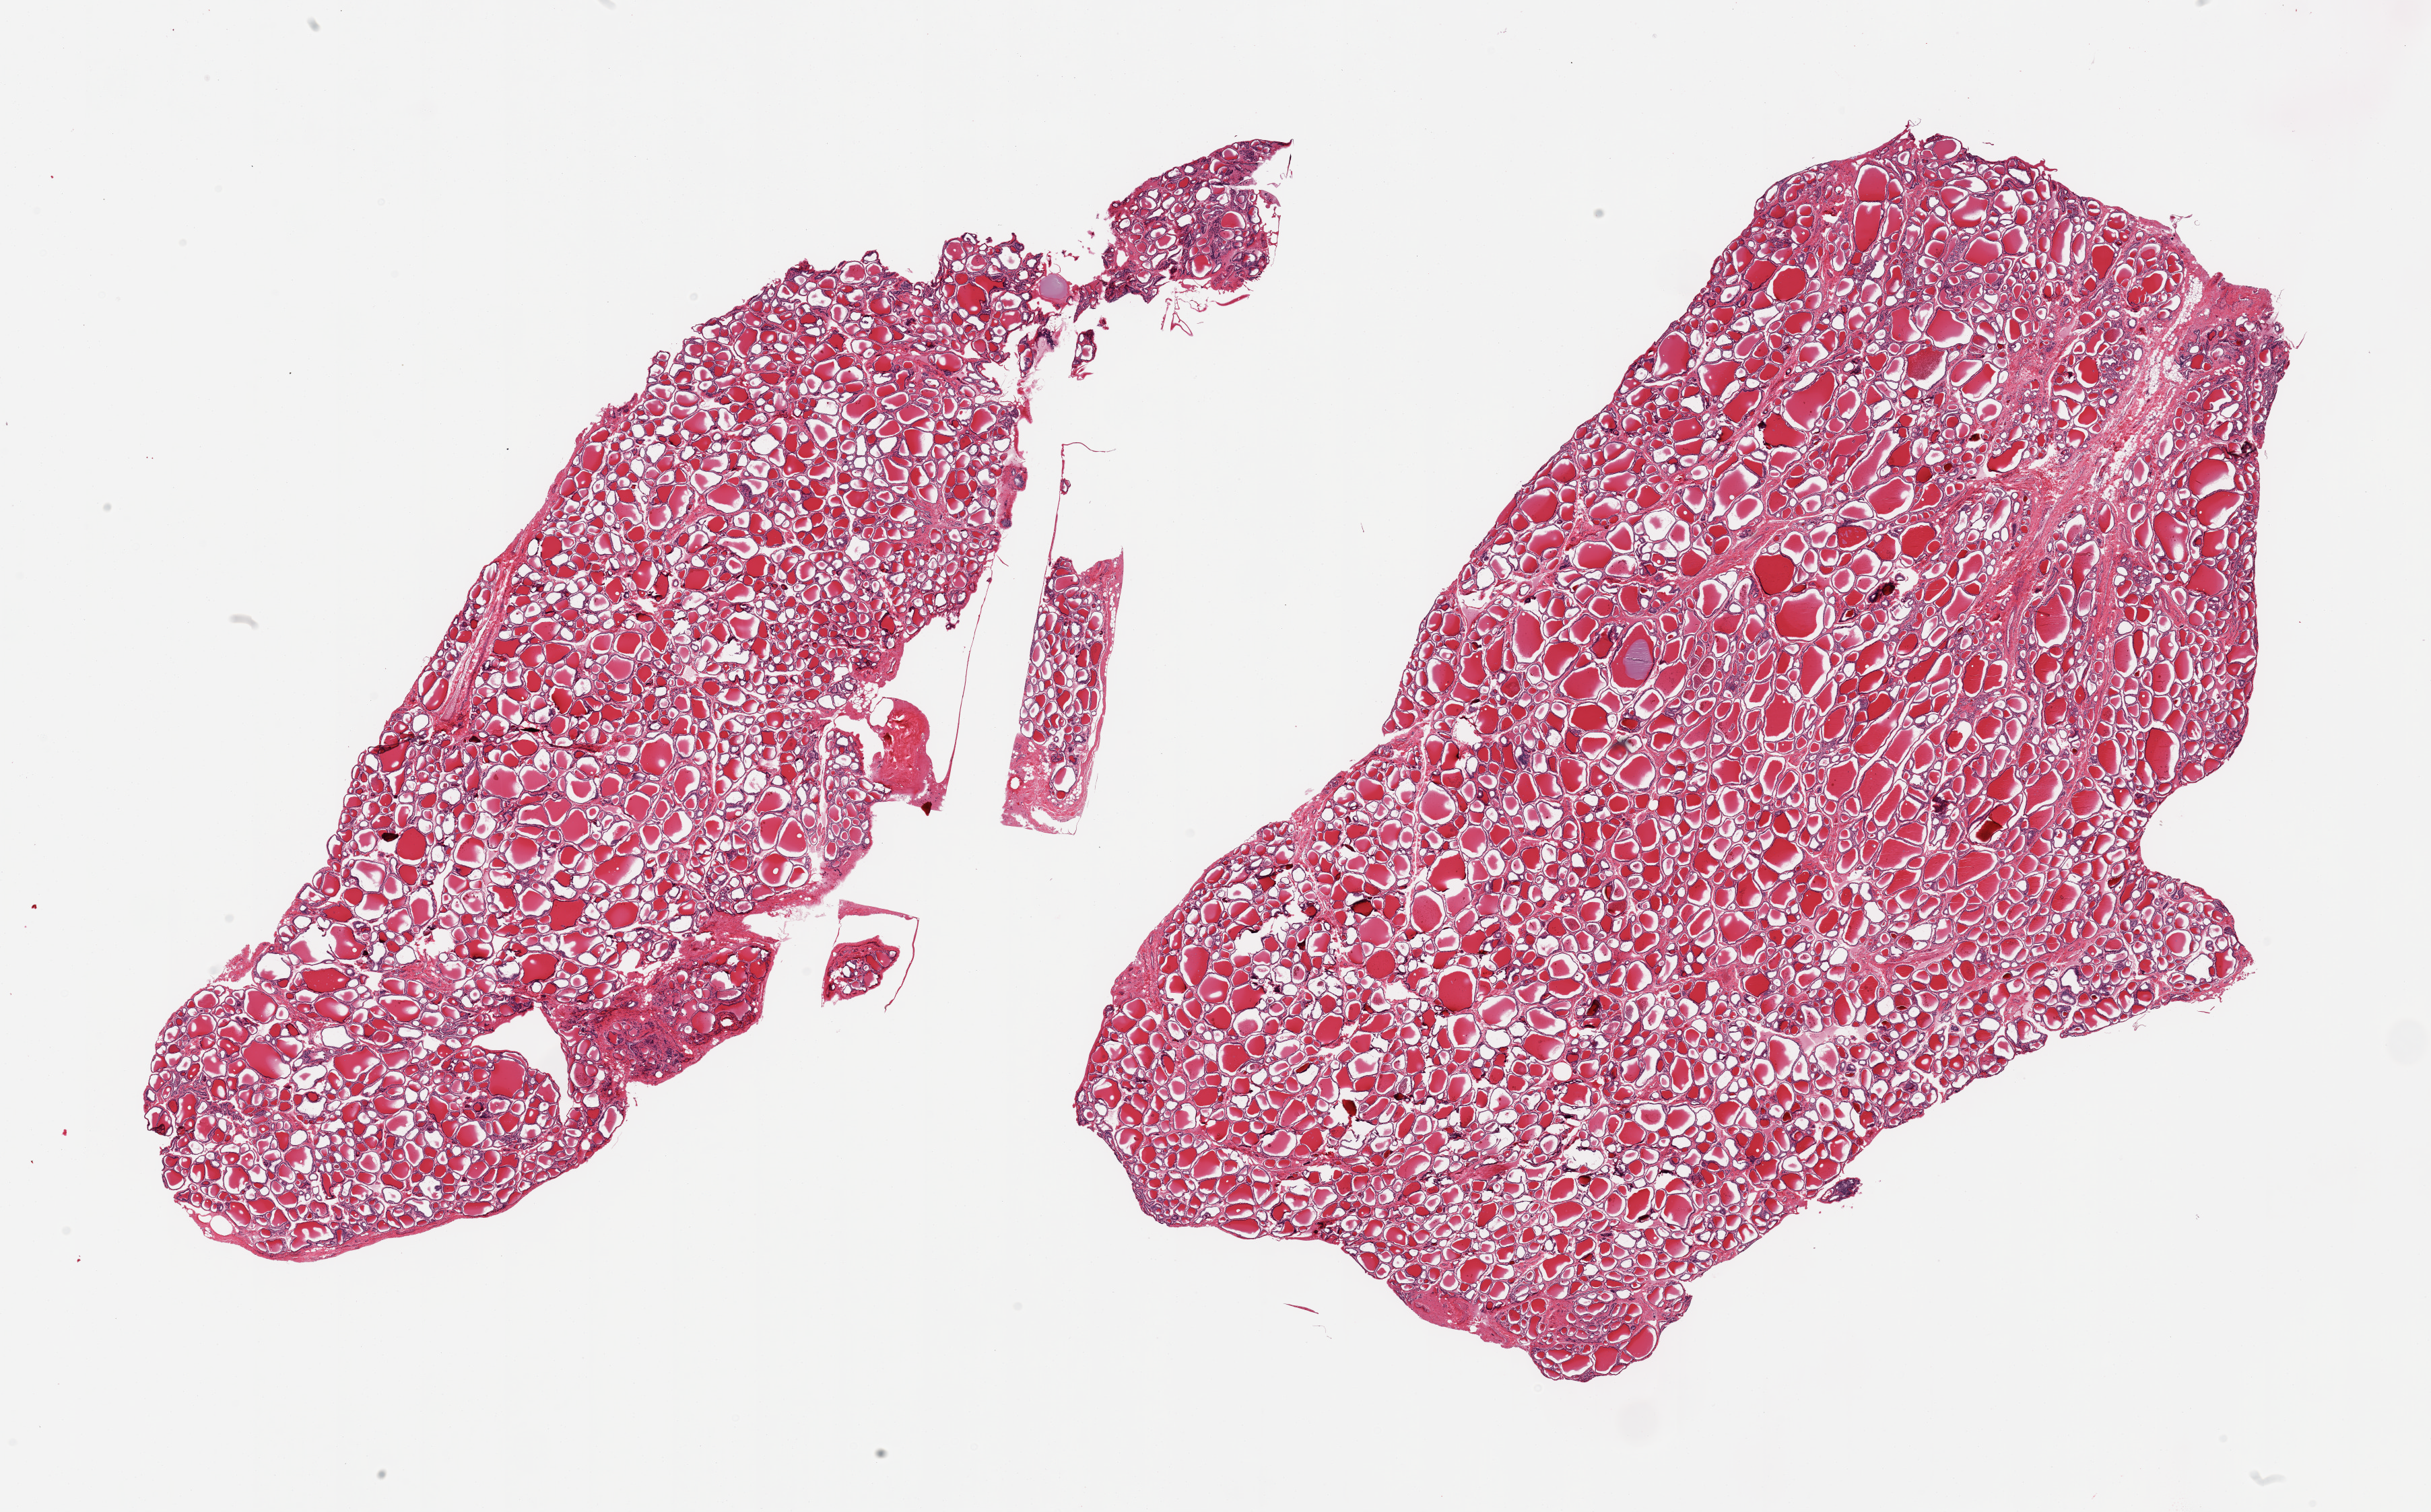
Digitized H&E-stained section — shown as a low-resolution overview of the whole scanned area (about 28.5 x 17.8 mm, from a 20x scan), PAXgene-fixed, paraffin-embedded tissue, section of thyroid (target tissue), tissue donor sample. Female donor.
* reviewer comment on this tissue sample: 2 pieces, no abnormalities